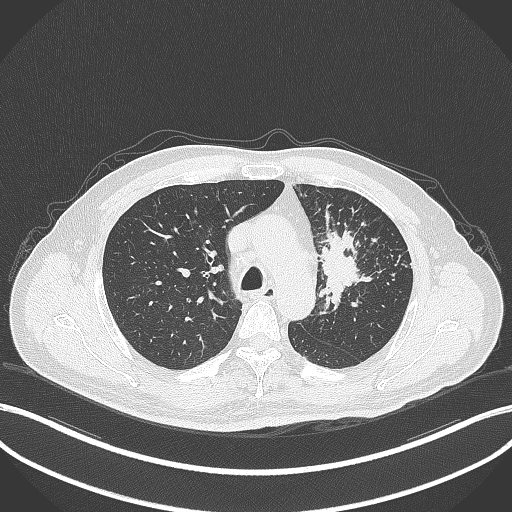
Chest CT, one axial slice. Position 249 of 386 along the scan axis. Lung window (W 1500 / L -600 HU). 1 mm slice thickness. 512 × 512 image matrix, field of view 400 × 400 mm. Patient: male, 69 years. From the clinical record (not read from this slice): clinical TNM (as recorded): T2a N2 M0; histopathological grade: G2-3.
Annotated regions visible in this slice (rectangle marked by the reading radiologist):
- lung tumour (recorded histology: adenocarcinoma): bounding box (x1, y1, x2, y2) in pixels: (311, 216, 369, 308)